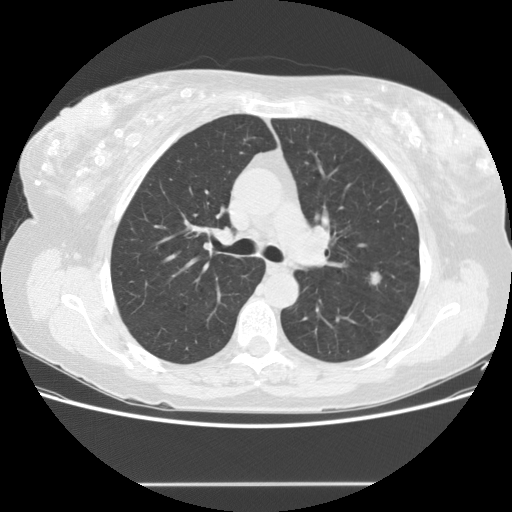
Low-dose screening chest CT, axial slice. Second annual screen. Lung window (W 1500 / L -600 HU). 2.5 mm slice thickness. Standard (soft-tissue) reconstruction kernel (STANDARD). Slice 53 of 151 in the series. Female, age 57 years at enrolment. Current smoker at enrolment.
Lesion marked by an expert reader, bounding box <358,263,392,294> (left, top, right, bottom; pixels). Screening reader's record for this exam (one nodule recorded; not confirmed to be the boxed lesion): non-calcified nodule or mass ≥4 mm, lingula, 10 × 8 mm, smooth margins, soft tissue attenuation, pre-existing on the prior screen: no. Official screen result: positive, other.